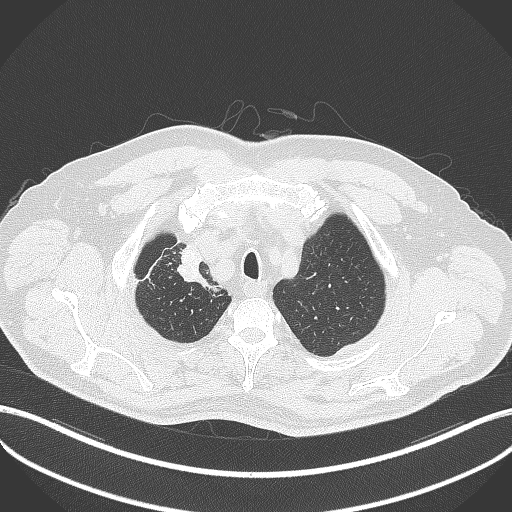
Chest CT, one axial slice; slice 334 of 411 in the series (ordered by position); lung window (W 1500 / L -600 HU); 512 × 512 image matrix. Patient: male, 60 years. From the clinical record (not read from this slice): clinical TNM (as recorded): T1b N1 M0.
Annotated regions visible in this slice (rectangle marked by the reading radiologist):
- lung tumour (recorded histology: squamous cell carcinoma): bounding box <179,244,222,293> (left, top, right, bottom; pixels)